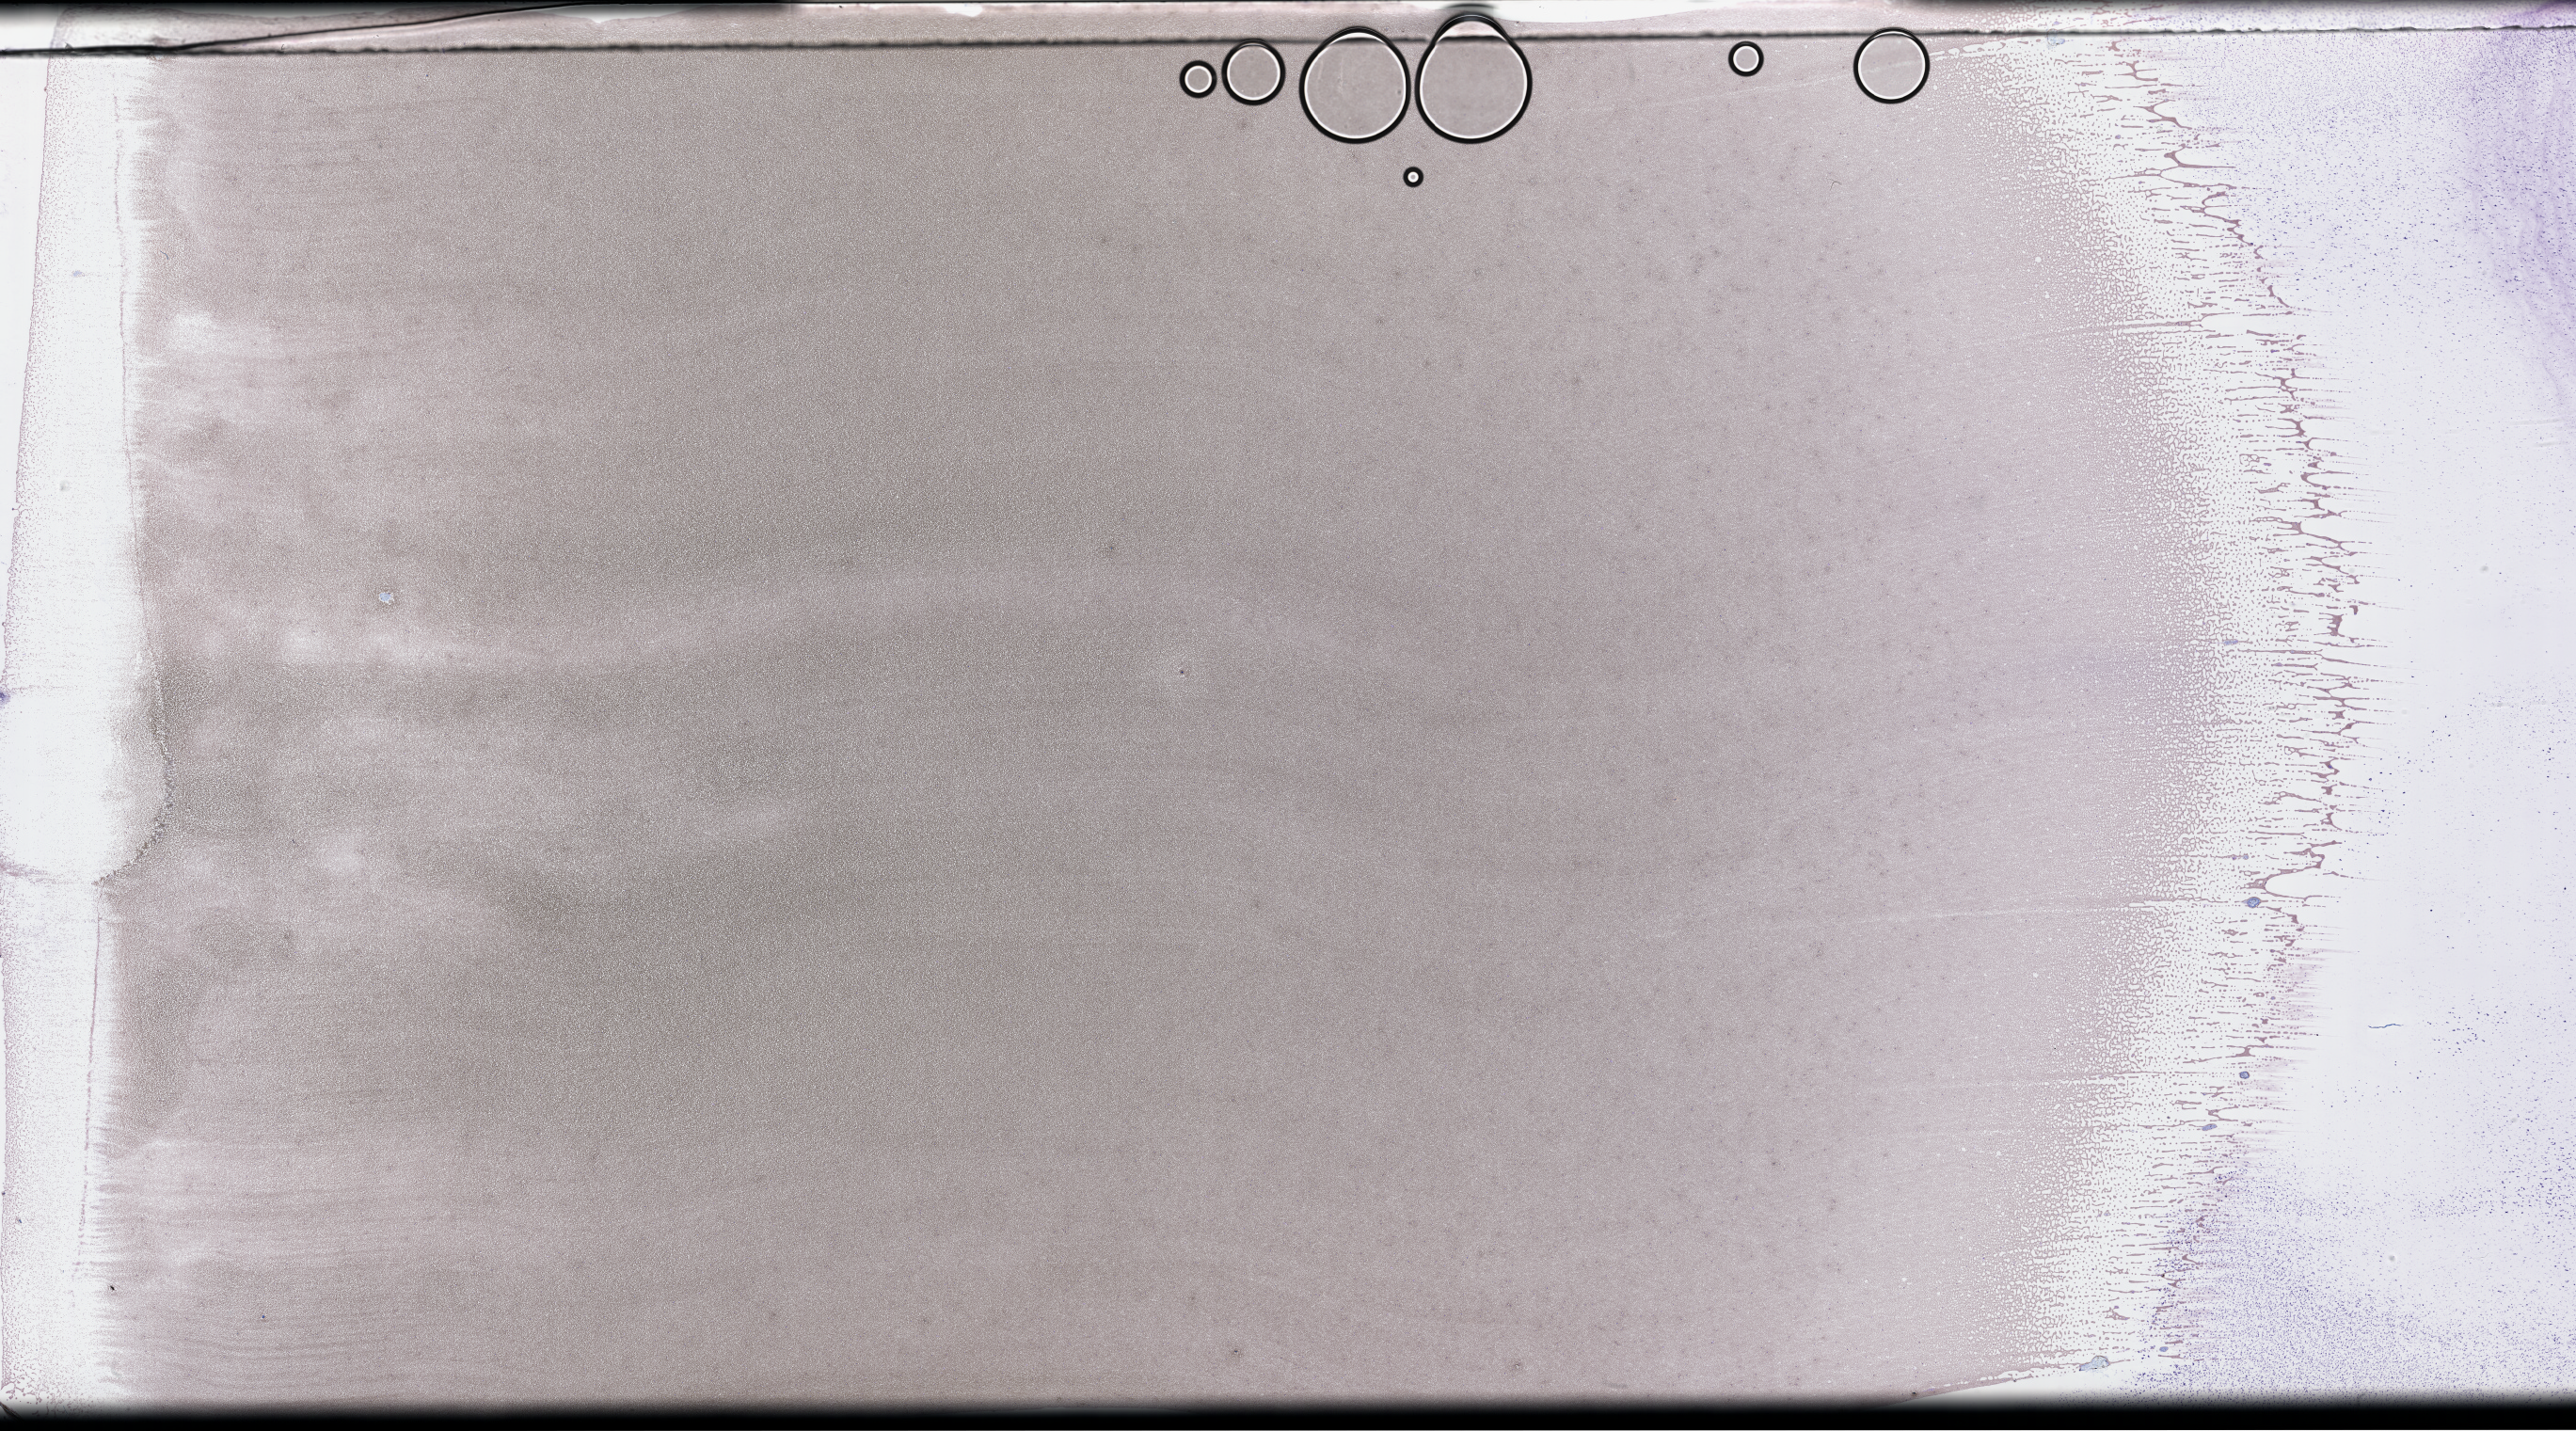
Wright–Giemsa-stained whole blood smear, whole-slide image, low-resolution overview of the scanned area, about 44.2 x 24.6 mm; specimen time point: collected on treatment. Patient sex: male.
Patient diagnosis: Plasma Cell Myeloma.